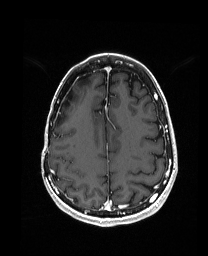
Brain MRI from a brain-tumour surgery series, one axial slice; position 56 of 192 along the scan axis; T1-weighted post-contrast; 1 mm slice thickness; 208 × 256 image matrix, field of view 203 × 250 mm. From the clinical record (not read from this slice): histopathology: Metastatic Carcinoma from Breast primary.
Outlined on this slice (outlined manually by an expert reader):
- previous resection cavity: bounding box (x1, y1, x2, y2) in pixels: (63, 90, 73, 106)